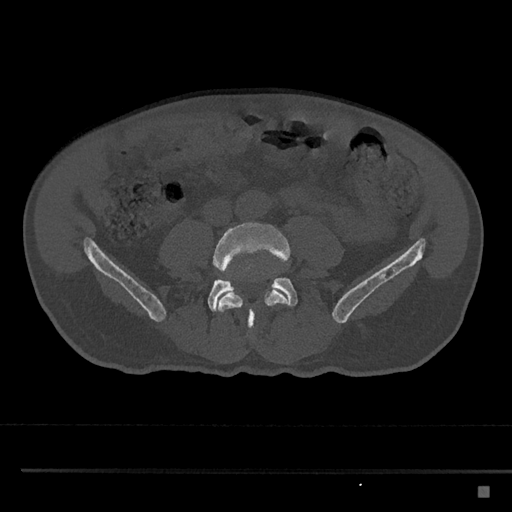
CT including the spine, one axial slice. Position 610 of 797 along the scan axis. Reconstruction kernel Br40s/3. 120 kVp. Bone window (W 1800 / L 400 HU). 0.5 mm slice thickness. 512 × 512 image matrix, field of view 391 × 391 mm. Patient: male, 59 years. Case-level facts recorded for this patient, not image findings: primary cancer: prostate.
Outlined on this slice (semi-automatically segmented with operator editing):
- L4 vertebra: box from (x=212, y=222) to (x=290, y=331) px
- L5 vertebra: (x=208, y=270)–(x=298, y=312)